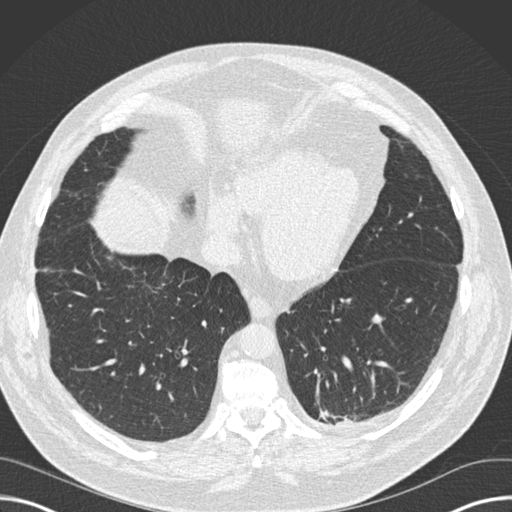
Low-dose screening chest CT, one axial slice. Slice 51 of 160 in the series (ordered by position). Reconstruction kernel B30f. Lung window (W 1500 / L -600 HU). 2 mm slice thickness. 512 × 512 image matrix, field of view 382 × 382 mm.
Outlined on this slice (outlined manually by an expert reader):
- lesion 1 (tumor, upper lobe of left lung): bounding box [x1, y1, x2, y2] px = [342, 418, 349, 424]